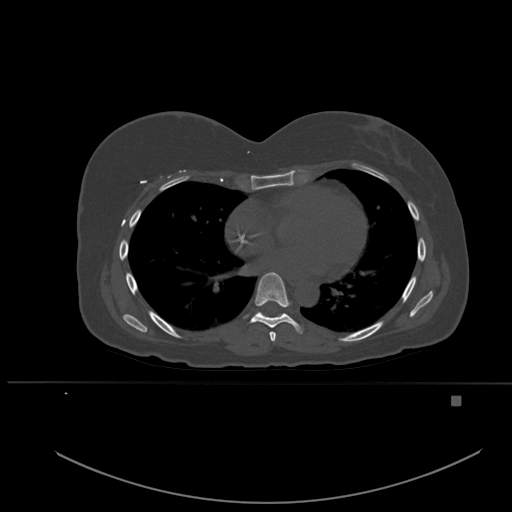
CT including the spine, one axial slice; position 335 of 651 along the scan axis; bone window (W 1800 / L 400 HU); 512 × 512 image matrix, field of view 443 × 443 mm. Female patient, age 49 years. From the clinical record (not read from this slice): primary cancer: breast; vertebrae with lytic lesions (as recorded): L3, T12, L4.
Outlined on this slice (semi-automatically segmented with operator editing):
- T6 vertebra: bounding box [x1, y1, x2, y2] px = [269, 331, 276, 342]
- T7 vertebra: [250, 272, 303, 334]
- T8 vertebra: [260, 312, 284, 314]